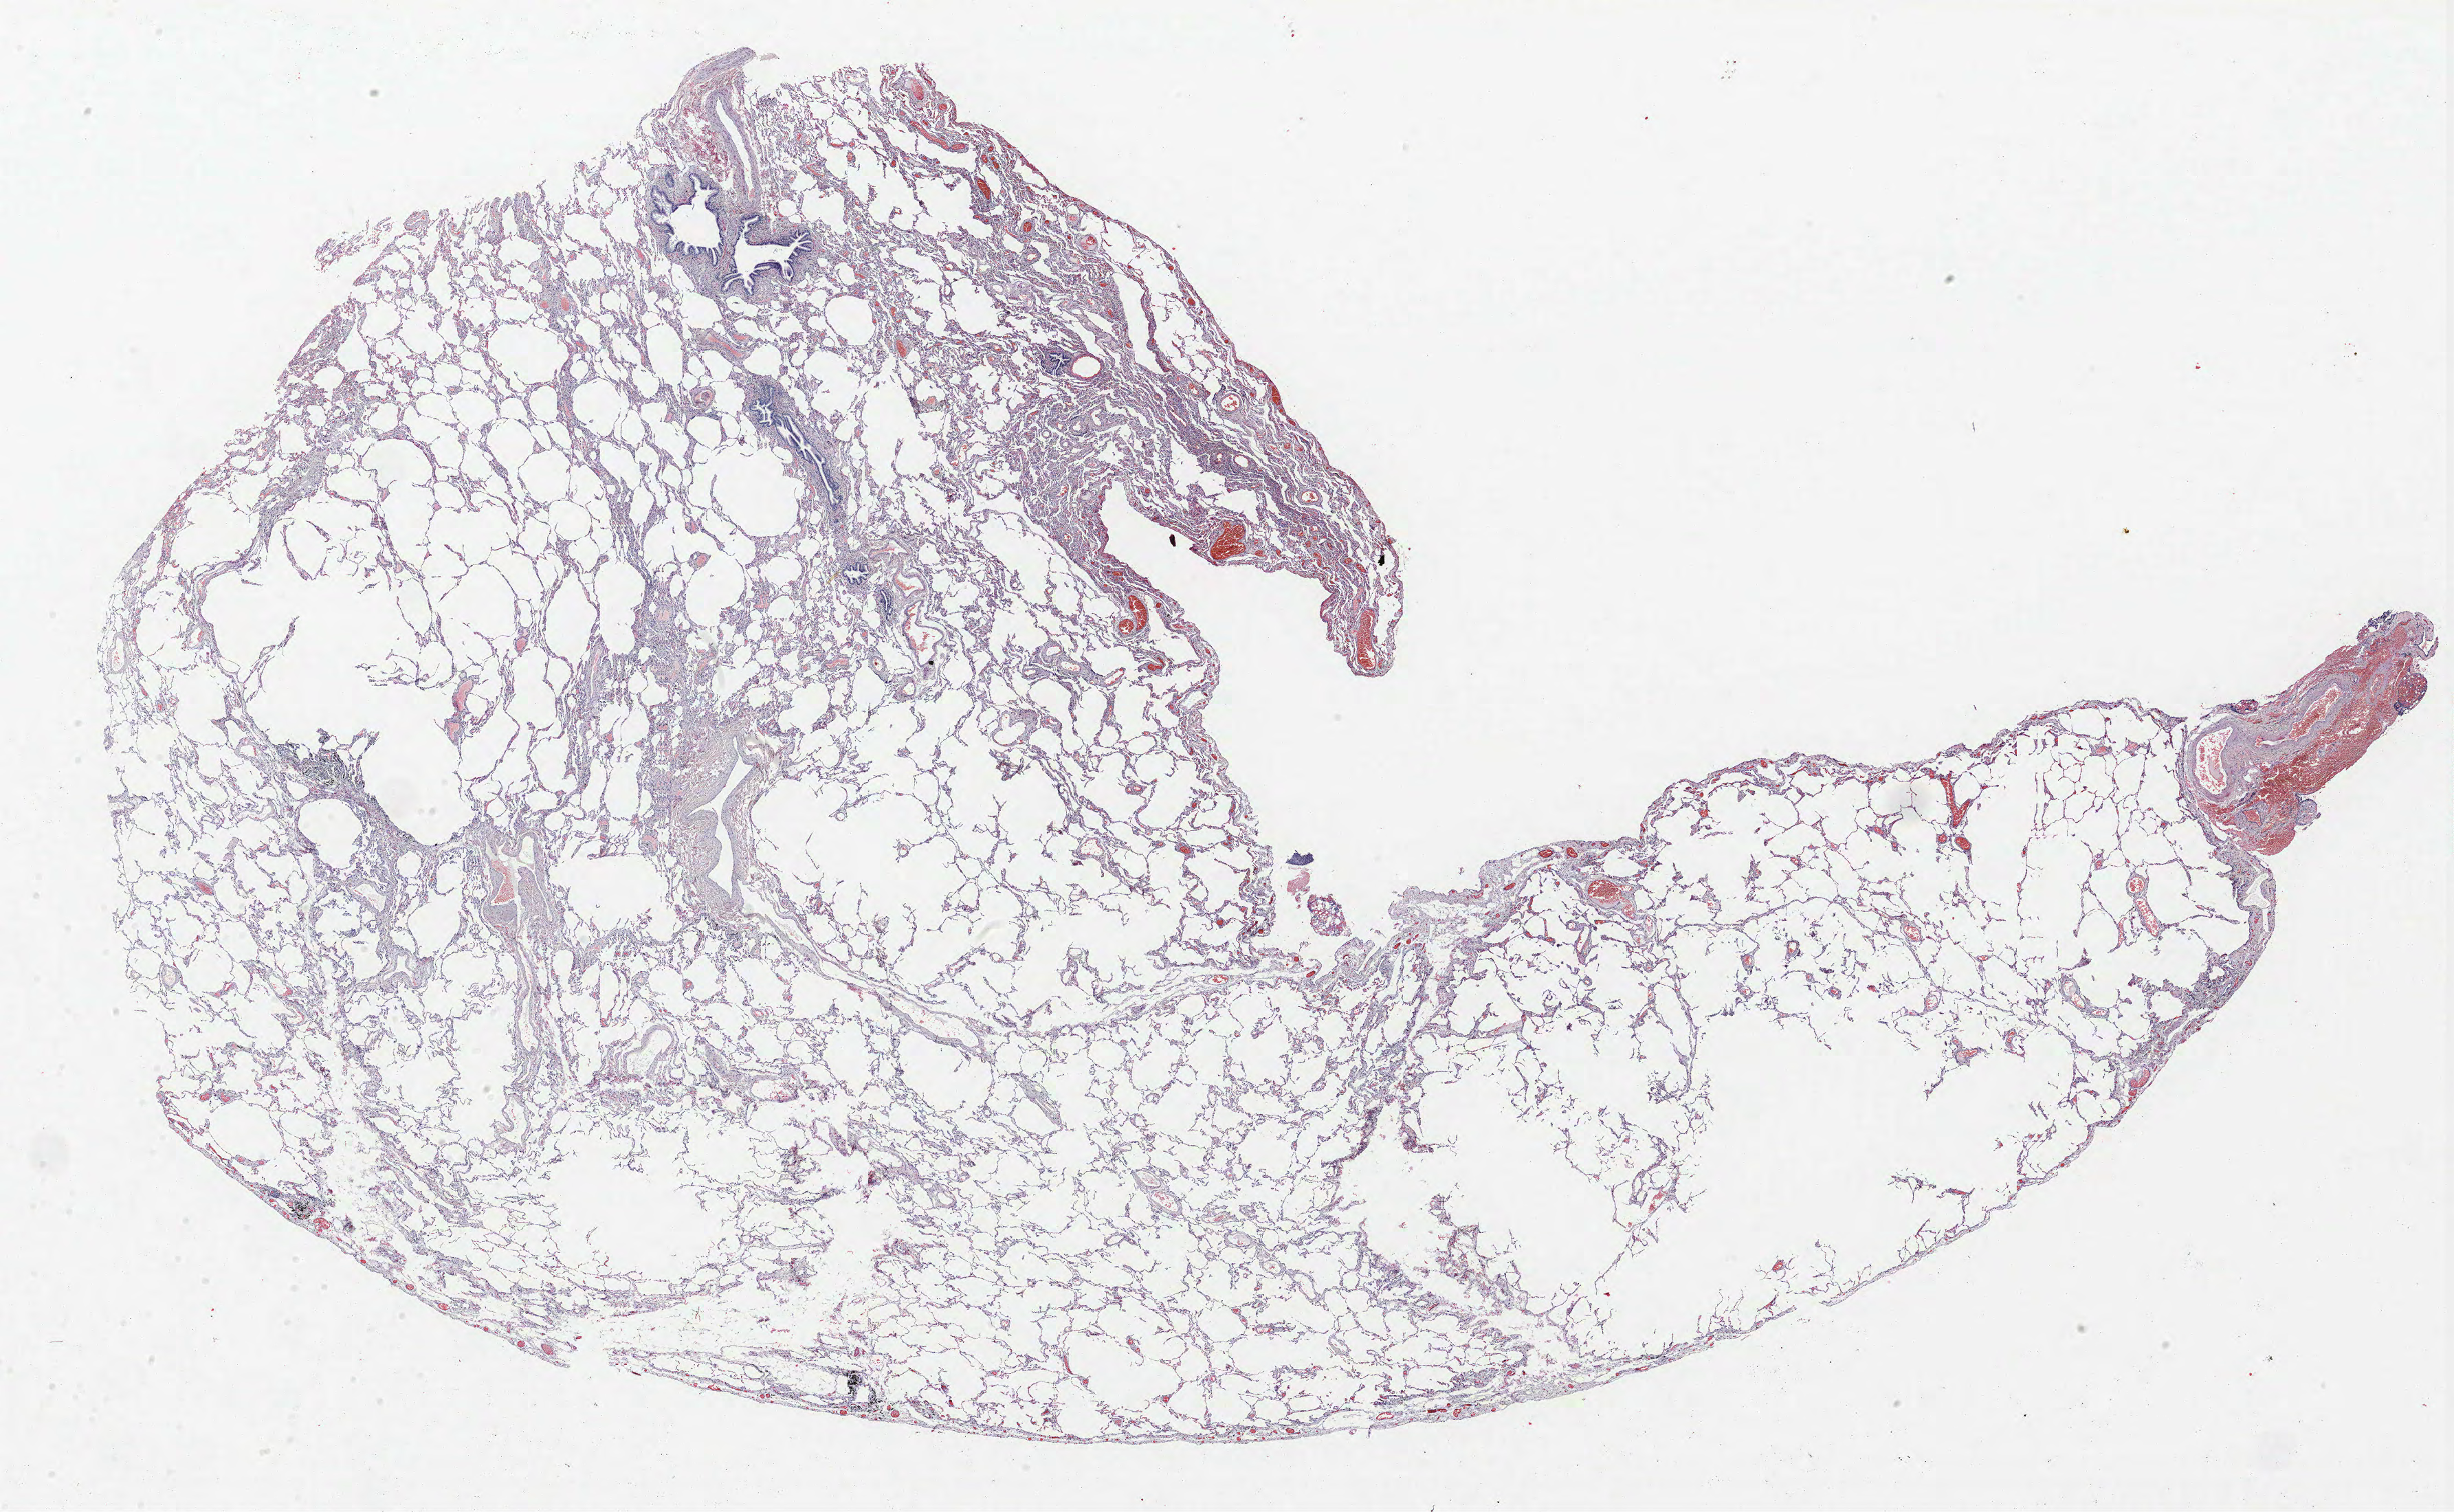
H&E whole-slide image — whole scanned area (about 28.6 x 17.6 mm) shown as a low-resolution overview; FFPE section; lung tissue. Male patient, aged 61 at enrolment.
Participant's lung-cancer diagnosis: Adenocarcinoma, NOS.